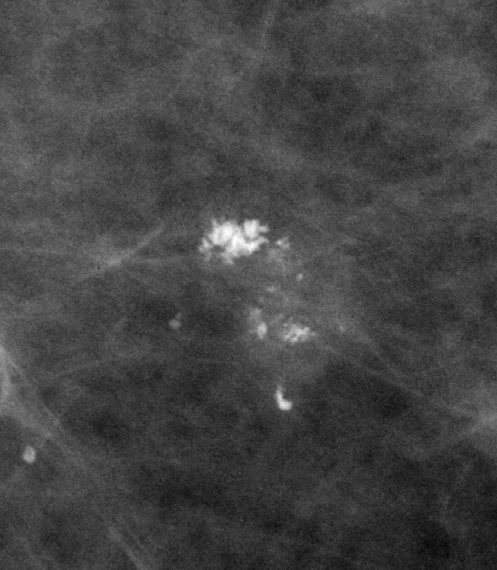
Region of interest cut from a scanned film mammogram (one marked finding), left breast, MLO view, BI-RADS breast density category 1 (scale 1–4).
Marked abnormality: calcifications, morphology pleomorphic, distribution clustered; BI-RADS assessment category 3; subtlety rating 5 on a 1 (subtle) to 5 (obvious) scale; pathology result (as recorded, not read from the image): benign.